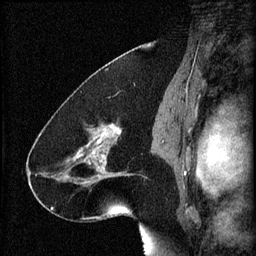
Breast MRI (dynamic contrast-enhanced), one sagittal slice; slice 38 of 60 in the series (ordered by position); 3 images stored at this slice position (order not interpretable as contrast timing); 1.5 T; TE 4.2 ms, TR 8.2 ms; 2 mm slice thickness; 256 × 256 image matrix, field of view 180 × 180 mm. Patient: female, 41 years.
Annotated regions visible in this slice (semi-automatically segmented with operator editing):
- analysis volume of interest (the breast-tissue region the enhancement analysis was run in; not a lesion): bounding box (x1, y1, x2, y2) in pixels: (72, 122, 134, 187)
- tumour enhancement mask (voxels above the 70 % enhancement threshold inside the analysis volume of interest): (76, 126, 122, 185)